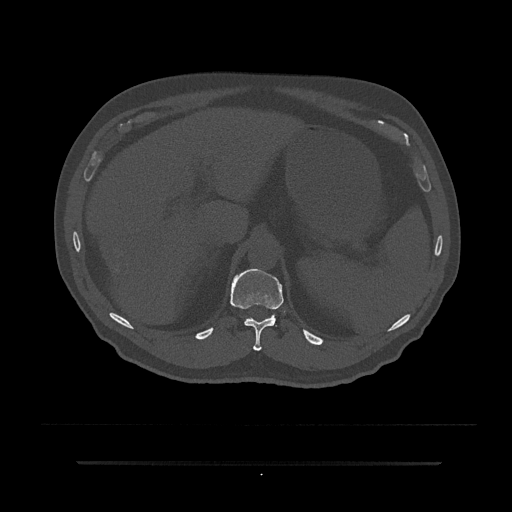
CT including the spine, one axial slice. Slice 257 of 797 in the series (ordered by position). Bone window (W 1800 / L 400 HU). 0.5 mm slice thickness. 512 × 512 image matrix, field of view 464 × 464 mm. Male patient, age 59 years. Case-level facts recorded for this patient, not image findings: primary cancer: bile ducts.
Structures marked on this image (semi-automatic segmentation, software-assisted and operator-edited):
- T11 vertebra: bounding box <230,268,284,351> (left, top, right, bottom; pixels)
- T12 vertebra: <245,316,276,321>